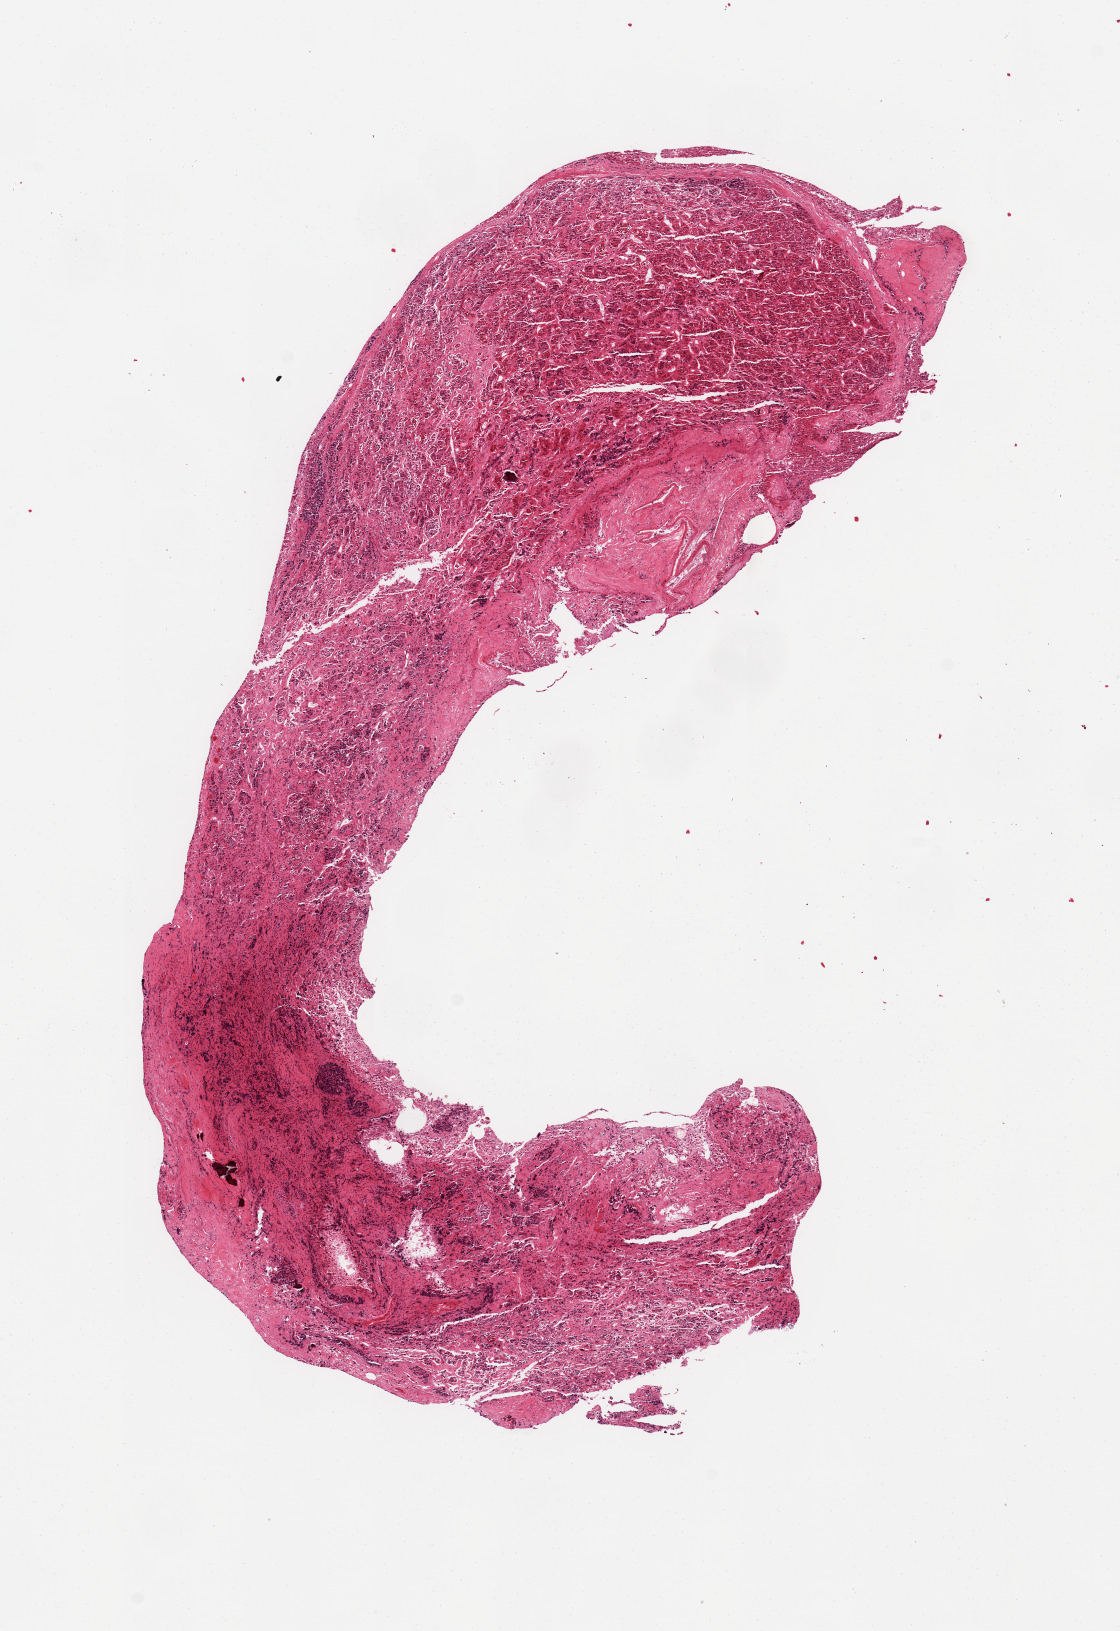
Digitized haematoxylin and eosin-stained section — shown as a low-resolution overview of the whole scanned area (about 8.9 x 12.9 mm, slide scanned at 20x); PAXgene-fixed, paraffin-embedded tissue; section of pituitary (target tissue); tissue donor sample. Donor: male.
Pathologist's review note for this sample: 1 pieces, badly autolyzed, apparent adenohypophysis.